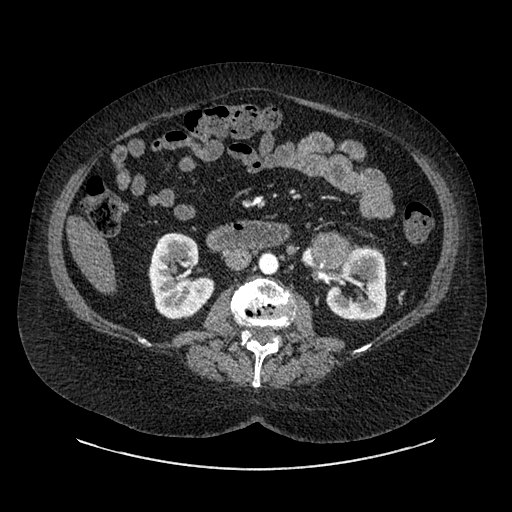
Contrast-enhanced abdominal CT, one axial slice. Slice 488 of 769 in the series (ordered by position). Soft-tissue window (W 400 / L 40 HU). 512 × 512 image matrix, field of view 460 × 460 mm. Female patient, age 61 years. From the clinical record (not read from this slice): diagnosis: adrenocortical carcinoma; tumour side: left adrenal; tumour size at pathology: 13 cm; Ki-67 index: 79 %; stage (as recorded): 2.
Annotated regions visible in this slice (semi-automatically segmented with operator editing):
- mass: bounding box <320,238,344,264> (left, top, right, bottom; pixels)